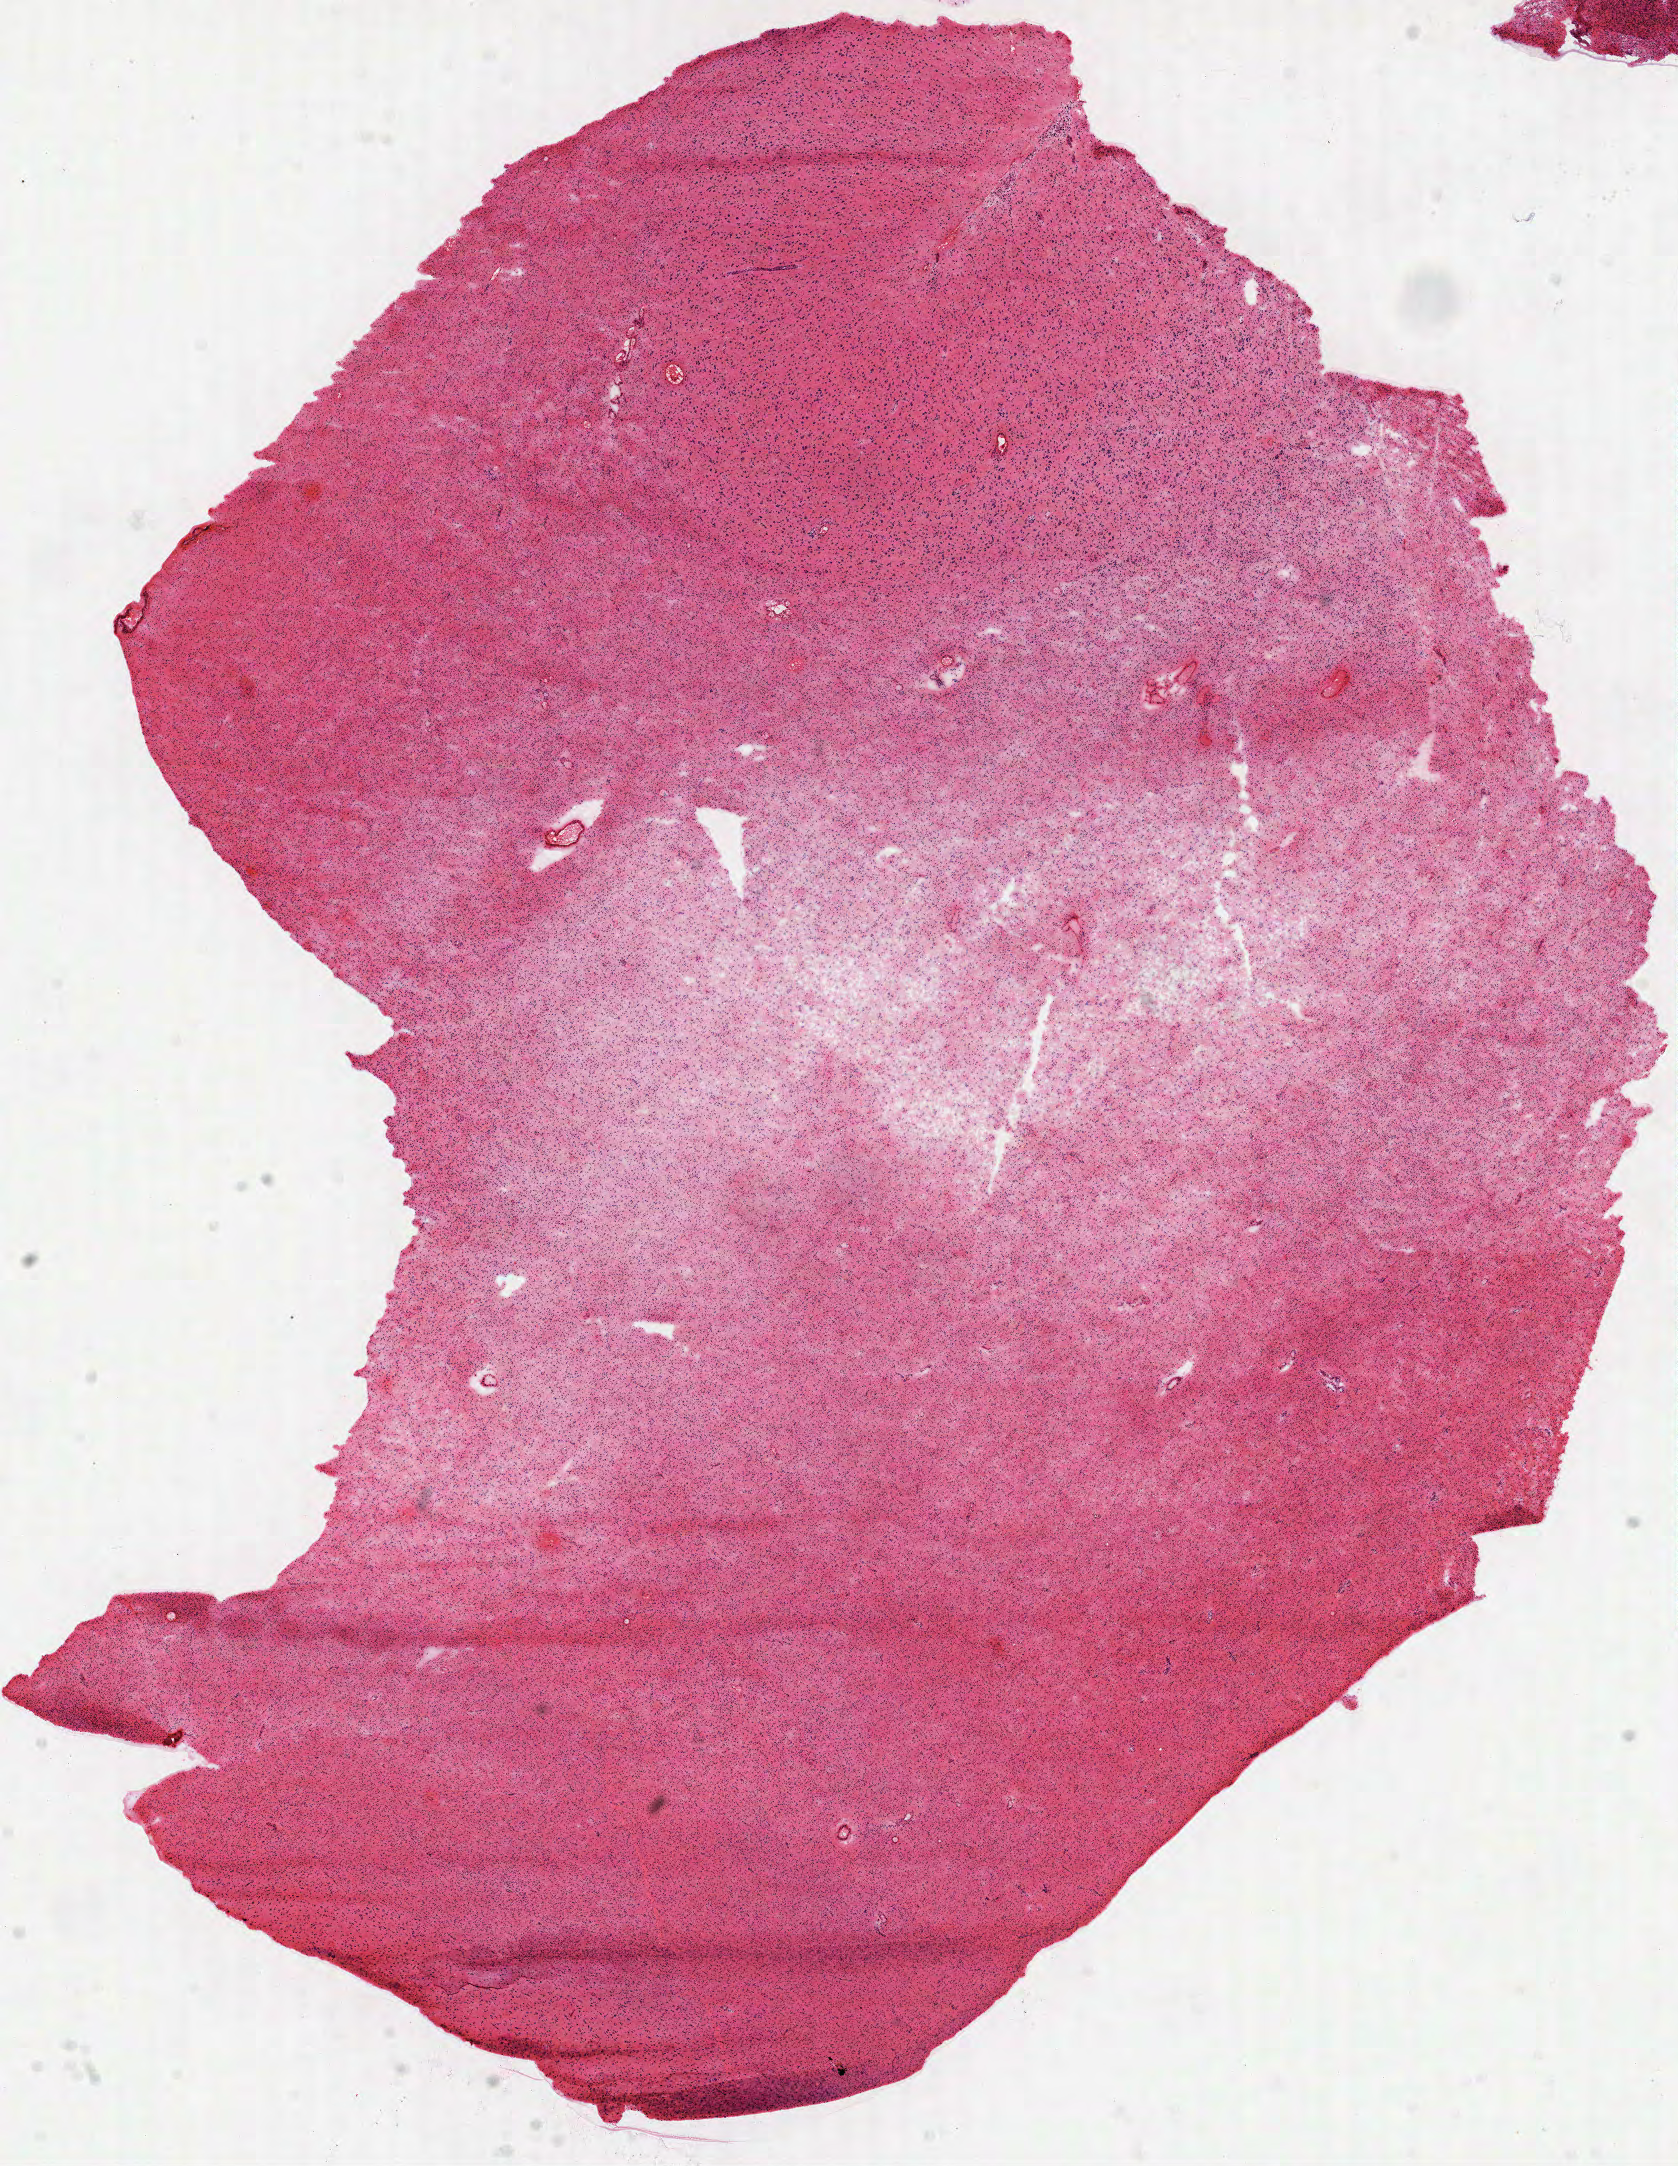
Whole-slide histology image, Hematoxylin and eosin (H&E) stained, shown as a low-resolution overview of the whole scanned area (about 13.5 x 17.5 mm, from a 40x scan). Frozen section. Primary tumour sample from the brain. Patient: female, age at initial diagnosis 45 years. Histologic grade: G2 (moderately differentiated). Composition of this section per pathologist review: tumour cells 100%, tumour nuclei 80%, normal cells 0%, stromal cells 0%, necrosis 0%.
• pathologic diagnosis: Oligodendroglioma, NOS (cerebrum)